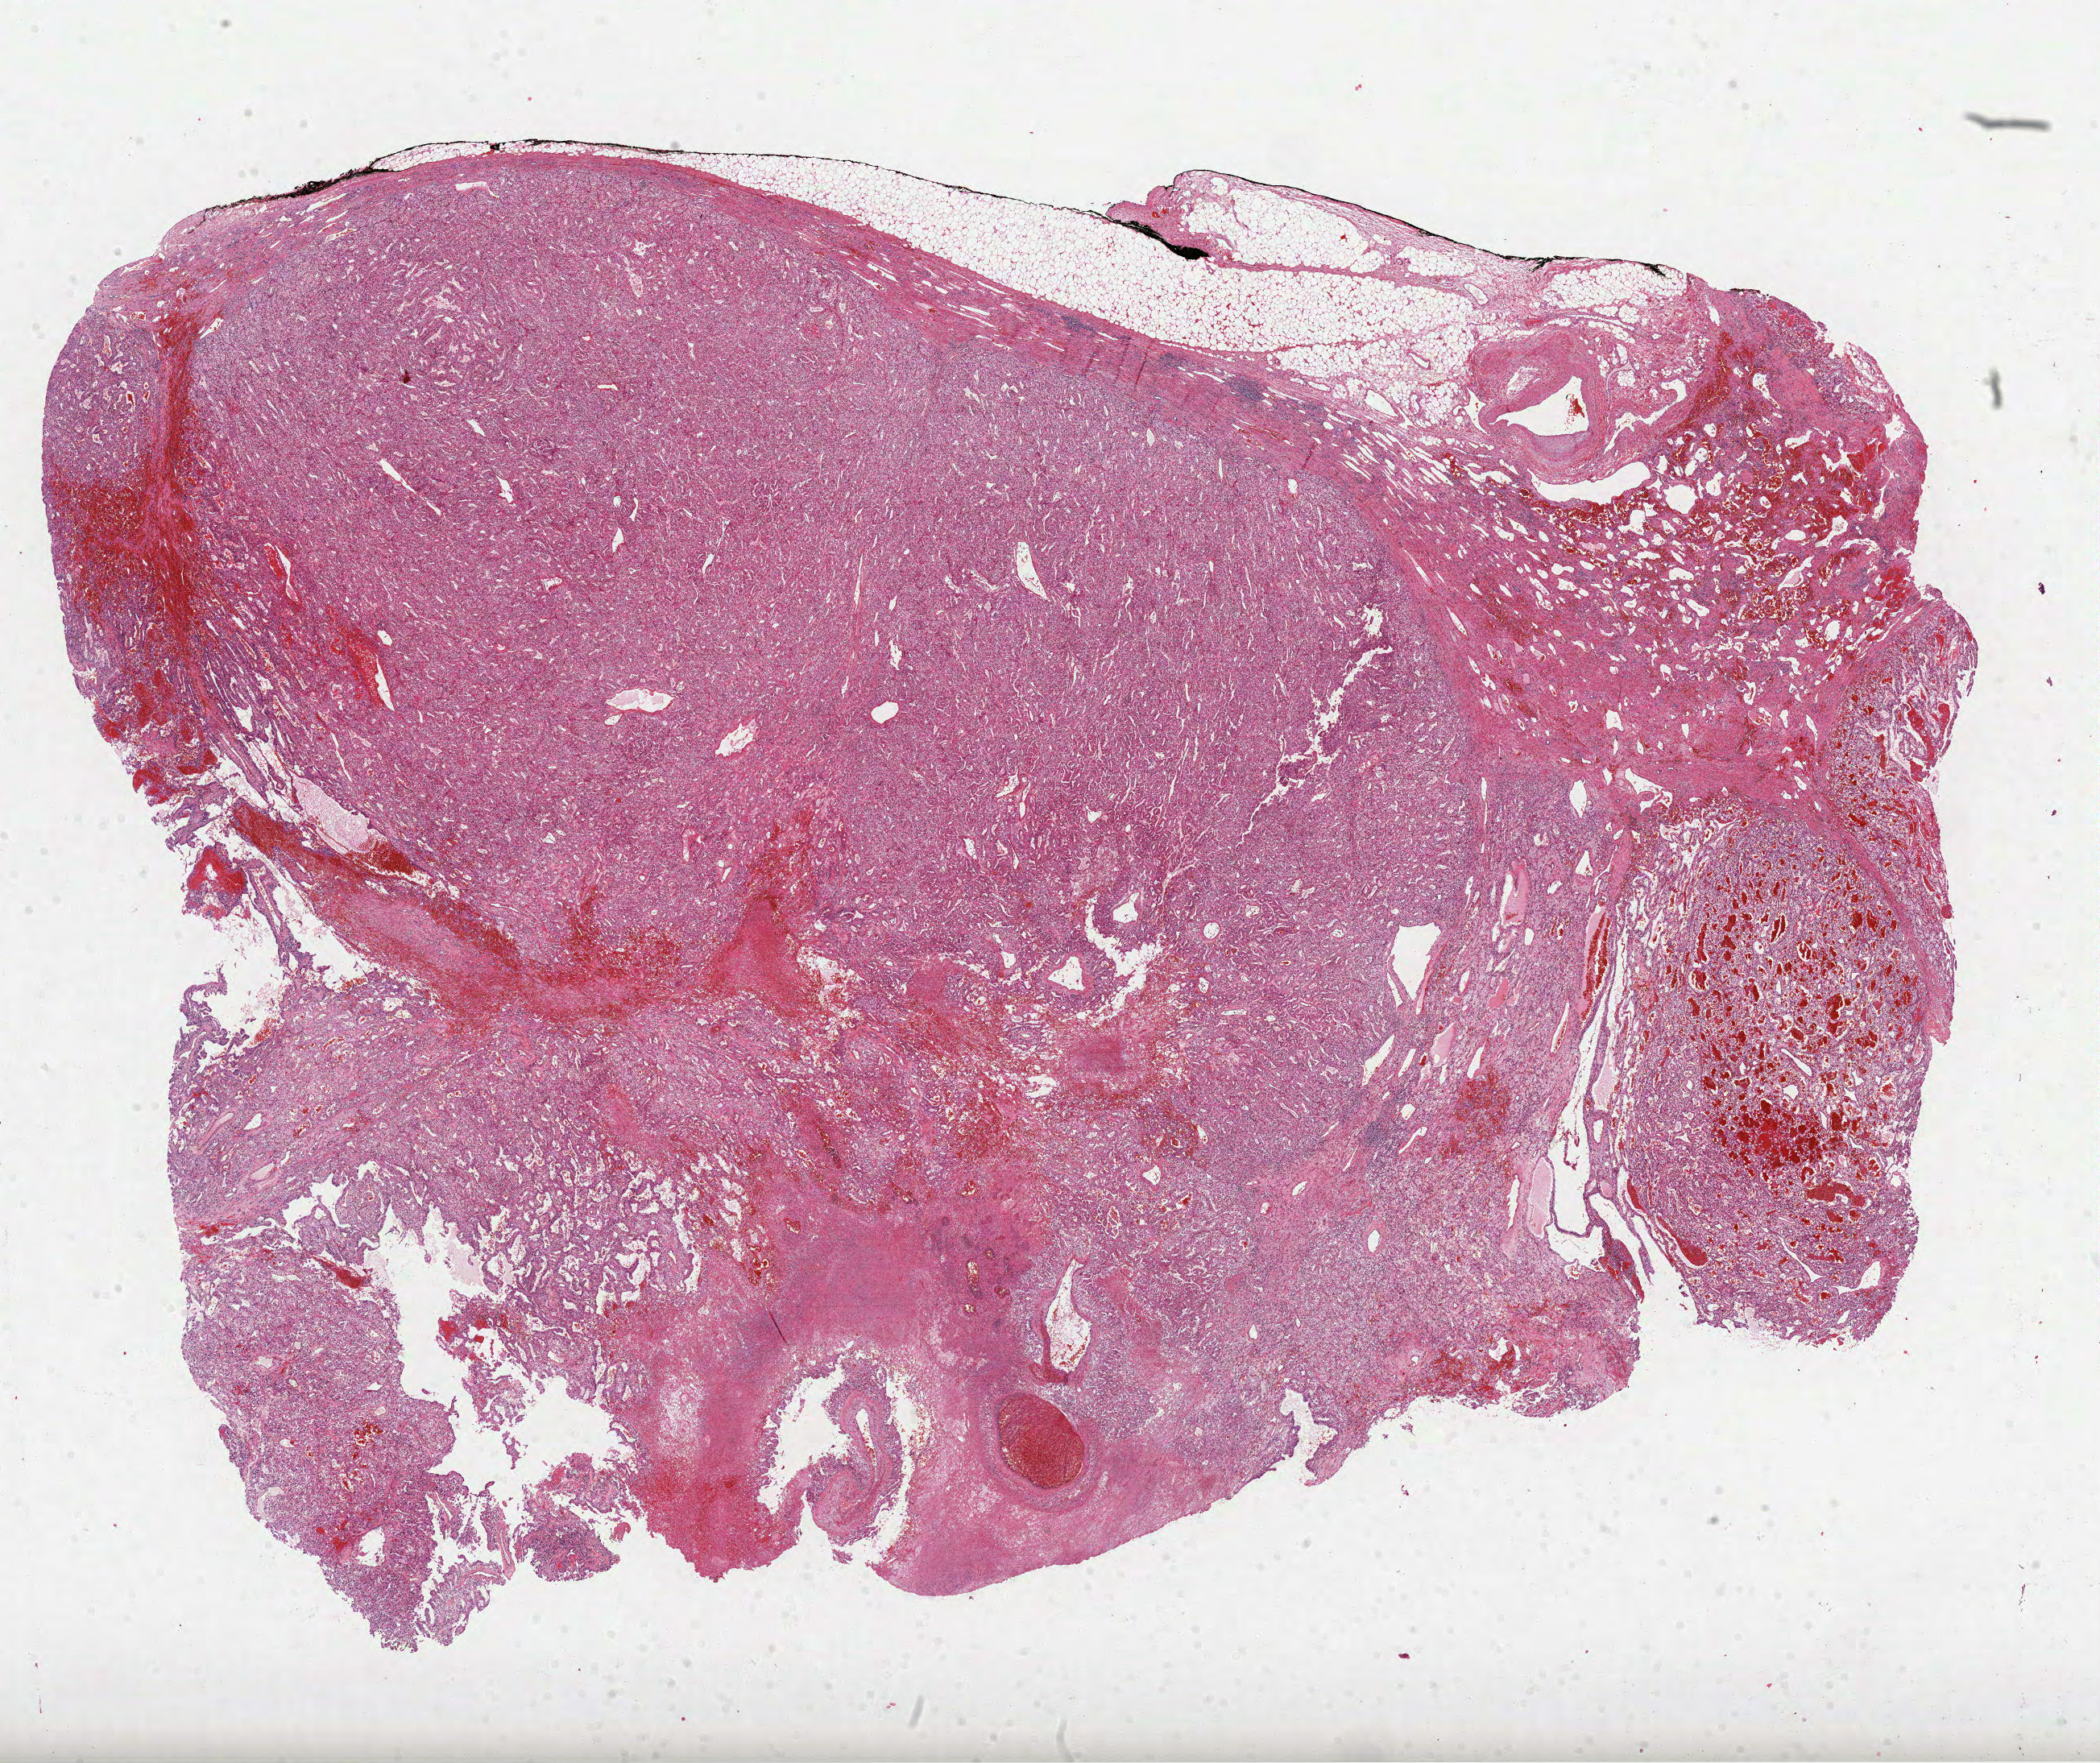
H&E whole-slide image — whole scanned area (about 21.0 x 17.7 mm, from a 40x scan) shown as a low-resolution overview, FFPE section, sample: primary tumour, kidney. Female, age 68 years at initial diagnosis. Histologic grade: G3 (poorly differentiated).
• laterality: left
• AJCC pathologic stage: III
• diagnosis: Clear cell adenocarcinoma, NOS
• lymph nodes positive (case pathology): 0 of 1 examined